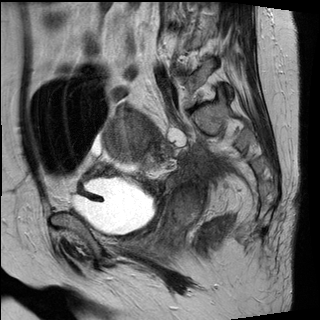
Pelvic MRI for cervical cancer, one sagittal slice. Position 11 of 30 along the scan axis. T2-weighted. 1.5 T. TE 89 ms, TR 2930 ms. 320 × 320 image matrix, field of view 260 × 260 mm. Patient: female, 62 years.
Annotated regions visible in this slice (outlined manually by an expert reader):
- uterus and cervix: box from (x=101, y=115) to (x=202, y=226) px